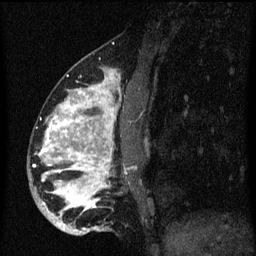
Breast MRI (dynamic contrast-enhanced), one sagittal slice. Position 23 of 60 along the scan axis. Dynamic contrast-enhanced series, image 2 of 3 at this slice position (ordered by acquisition). 1.5 T. TE 4.2 ms, TR 8.4 ms. 2 mm slice thickness. 256 × 256 image matrix, field of view 180 × 180 mm. Female patient, age 34 years. From the clinical record (not read from this slice): setting: breast cancer imaged before/during neoadjuvant chemotherapy; receptor status: HR-positive, HER2-negative.
Outlined on this slice (semi-automatically segmented with operator editing):
- analysis volume of interest (the breast-tissue region the enhancement analysis was run in; not a lesion): bounding box [x1, y1, x2, y2] px = [28, 58, 137, 237]
- tumour enhancement mask (voxels above the 70 % enhancement threshold inside the analysis volume of interest): [40, 70, 117, 229]